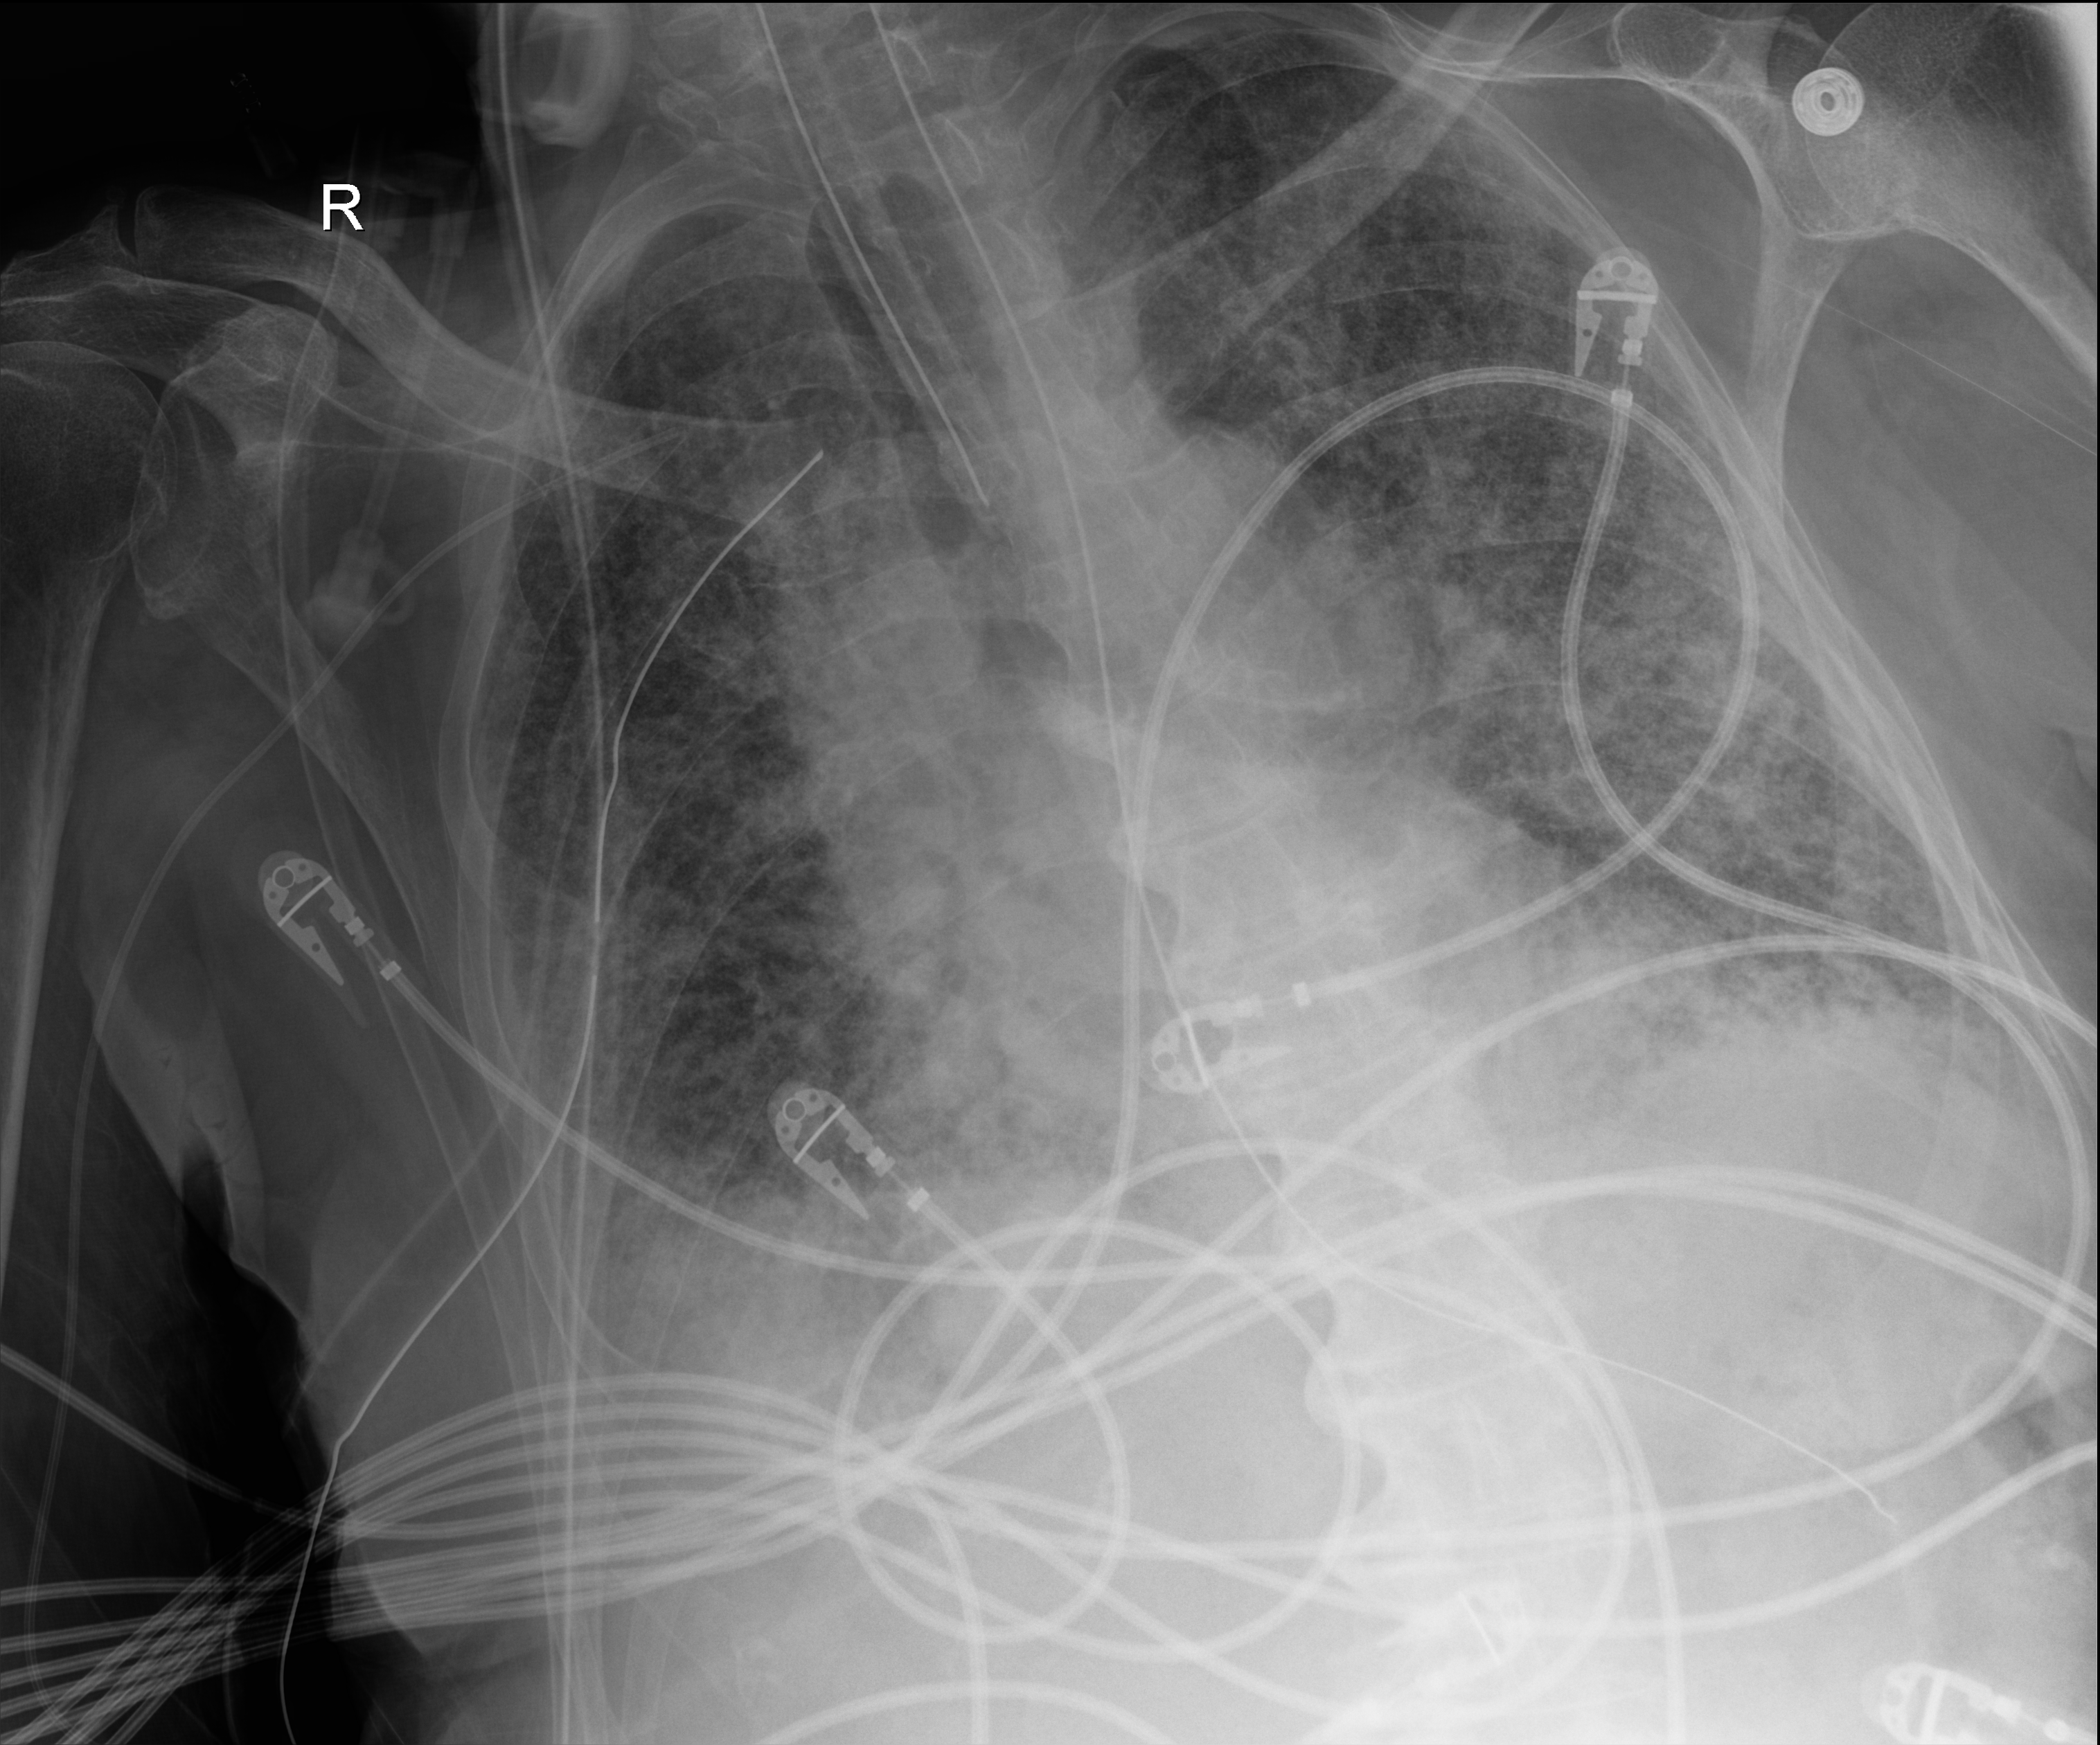
Chest X-ray (portable); anteroposterior (AP) projection. Male patient hospitalised with COVID-19, age 75–90 years.
From the hospital-stay record, not from the radiograph (when in the stay this image was taken is not recorded): diabetes (admission record): no; length of hospital stay: 47 days; mechanically ventilated during this hospital stay: yes.